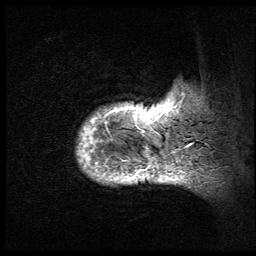
Breast MRI (dynamic contrast-enhanced), one sagittal slice. Slice 6 of 64 in the series (ordered by position). 3 images stored at this slice position (order not interpretable as contrast timing). 1.5 T. TE 4.2 ms, TR 9 ms. 2.5 mm slice thickness. 256 × 256 image matrix, field of view 180 × 180 mm. Female patient, age 50 years. Case-level facts recorded for this patient, not image findings: setting: breast cancer imaged before/during neoadjuvant chemotherapy; receptor status: triple-negative.
Structures marked on this image (semi-automatic segmentation, software-assisted and operator-edited):
- analysis volume of interest (the breast-tissue region the enhancement analysis was run in; not a lesion): bounding box <62,73,194,211> (left, top, right, bottom; pixels)
- tumour enhancement mask (voxels above the 140 % enhancement threshold inside the analysis volume of interest): <78,101,189,185>